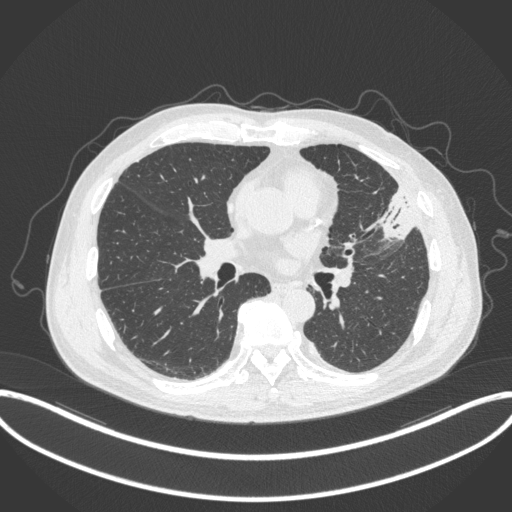
Chest CT, one axial slice; slice 168 of 382 in the series (ordered by position); 120 kVp; lung window (W 1500 / L -600 HU); 1 mm slice thickness; 512 × 512 image matrix. Patient: male, 64 years. Case-level facts recorded for this patient, not image findings: clinical TNM (as recorded): T4 N1 M0.
Outlined on this slice (bounding box drawn by a radiologist):
- lung tumour (recorded histology: adenocarcinoma): bounding box (x1, y1, x2, y2) in pixels: (380, 186, 415, 243)